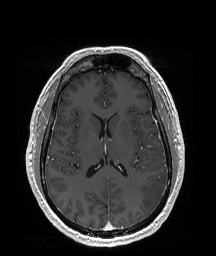
Brain MRI from a brain-tumour surgery series, one axial slice. Slice 89 of 192 in the series (ordered by position). T1-weighted post-contrast. 1 mm slice thickness. 216 × 256 image matrix, field of view 219 × 260 mm. Case-level facts recorded for this patient, not image findings: histopathology: Glioblastoma; WHO grade: 4; IDH mutation: no; tumour location: Left Temporal Parietal.
Structures marked on this image (manually delineated by an expert):
- tumour: bounding box (x1, y1, x2, y2) in pixels: (140, 176, 167, 210)